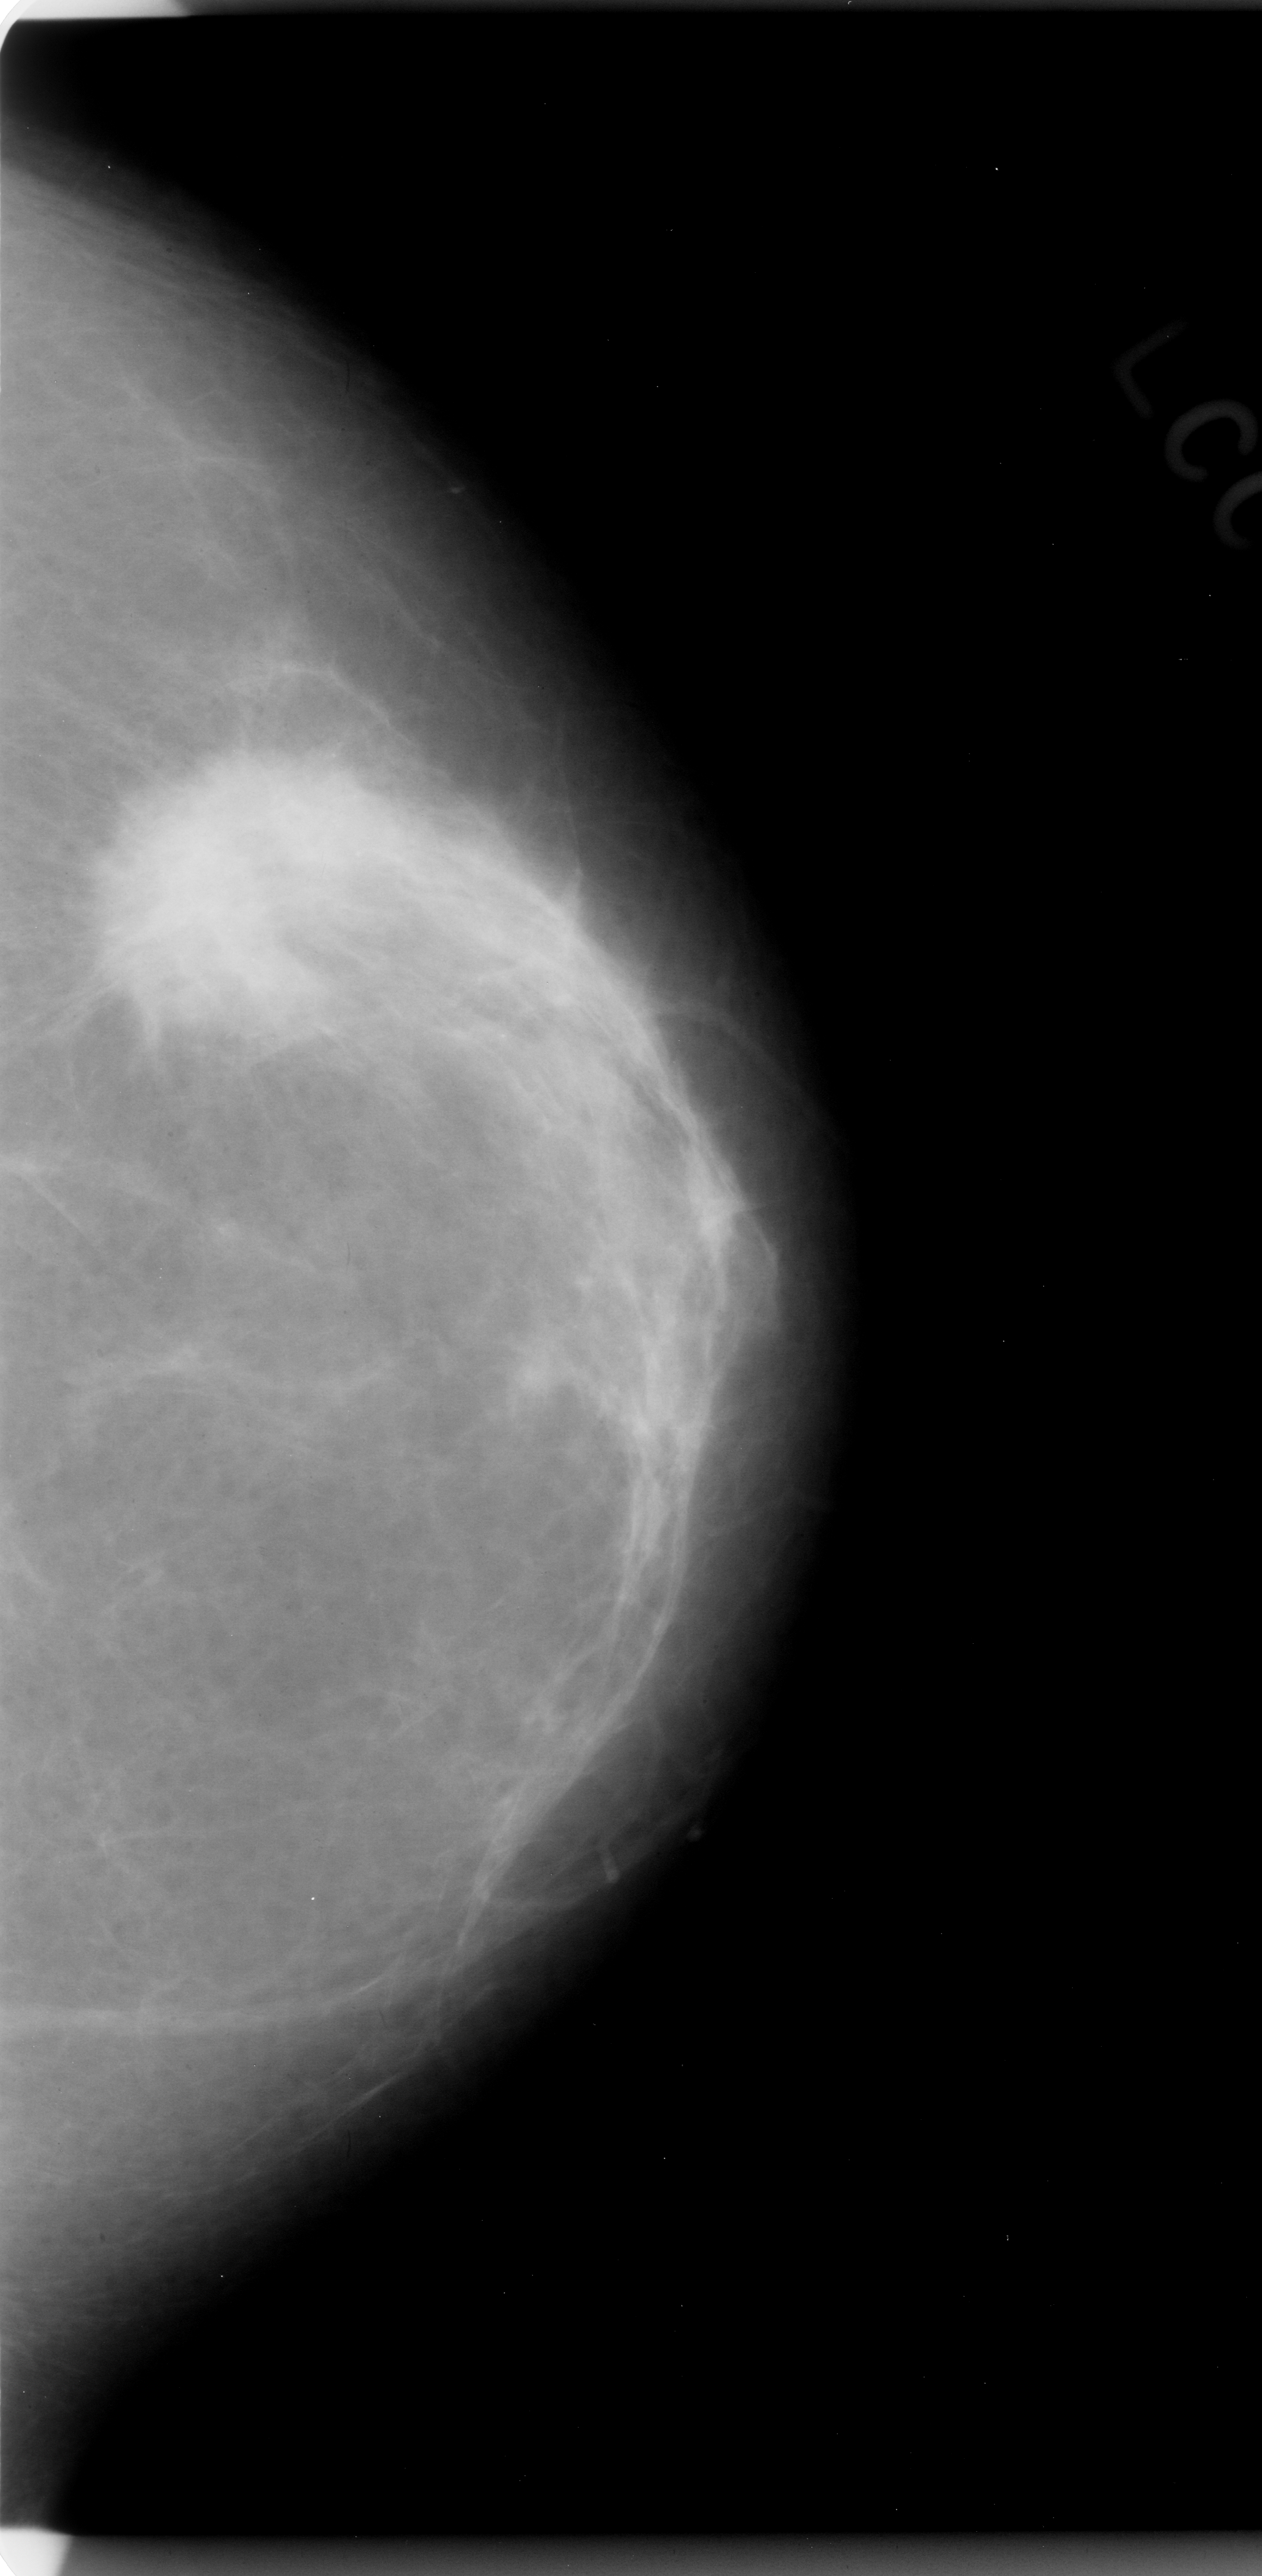
Scanned film-screen mammogram. Left breast. Craniocaudal (CC) view. 1262 × 2576 image matrix.
Expert-marked regions of interest on this film, with their recorded descriptors:
- mass, shape irregular, margins spiculated; BI-RADS assessment category 5; subtlety rating 5 on a 1 (subtle) to 5 (obvious) scale; pathology (as recorded): malignant: bounding box [x1, y1, x2, y2] px = [61, 729, 326, 1022]